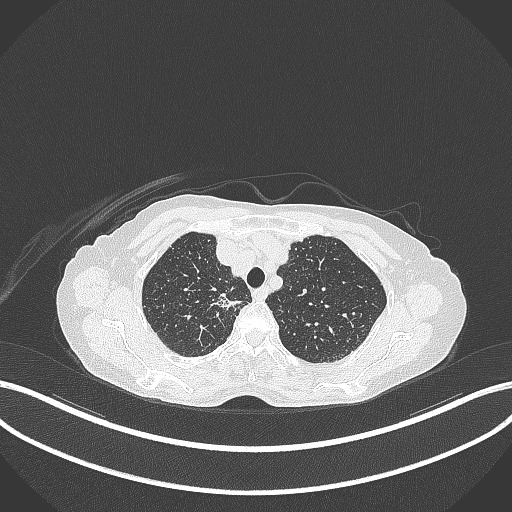
Chest CT, one axial slice. Position 304 of 403 along the scan axis. Reconstruction kernel B70f. 120 kVp. Lung window (W 1500 / L -600 HU). 1 mm slice thickness. 512 × 512 image matrix, field of view 400 × 400 mm. Female patient, age 75 years. Case-level facts recorded for this patient, not image findings: clinical TNM (as recorded): T1c N1 M1.
Annotated regions visible in this slice (rectangle marked by the reading radiologist):
- lung tumour (recorded histology: adenocarcinoma): bounding box <210,289,246,317> (left, top, right, bottom; pixels)